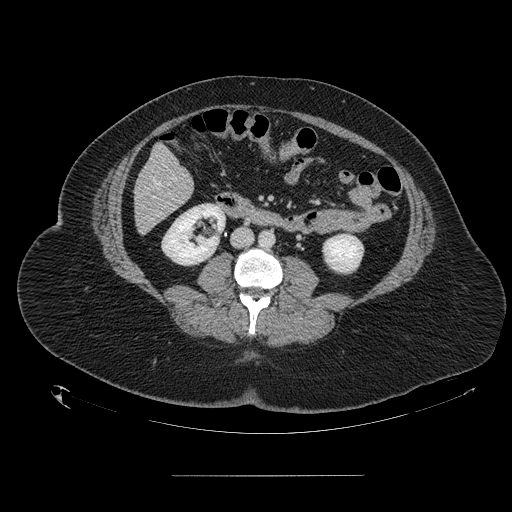
Contrast-enhanced abdominal CT, one axial slice; position 37 of 164 along the scan axis; intravenous contrast given; soft-tissue window (W 400 / L 40 HU); 2.5 mm slice thickness; 512 × 512 image matrix, field of view 495 × 495 mm. Female patient, age 52 years. Case-level facts recorded for this patient, not image findings: diagnosis: colorectal cancer liver metastases, imaged before liver resection; multiple liver metastases: yes; largest metastasis: 3.5 cm; disease in both lobes: no.
Outlined on this slice (outlined manually by an expert reader):
- hepatic veins: bounding box (x1, y1, x2, y2) in pixels: (153, 179, 161, 186)
- liver: (135, 146, 193, 232)